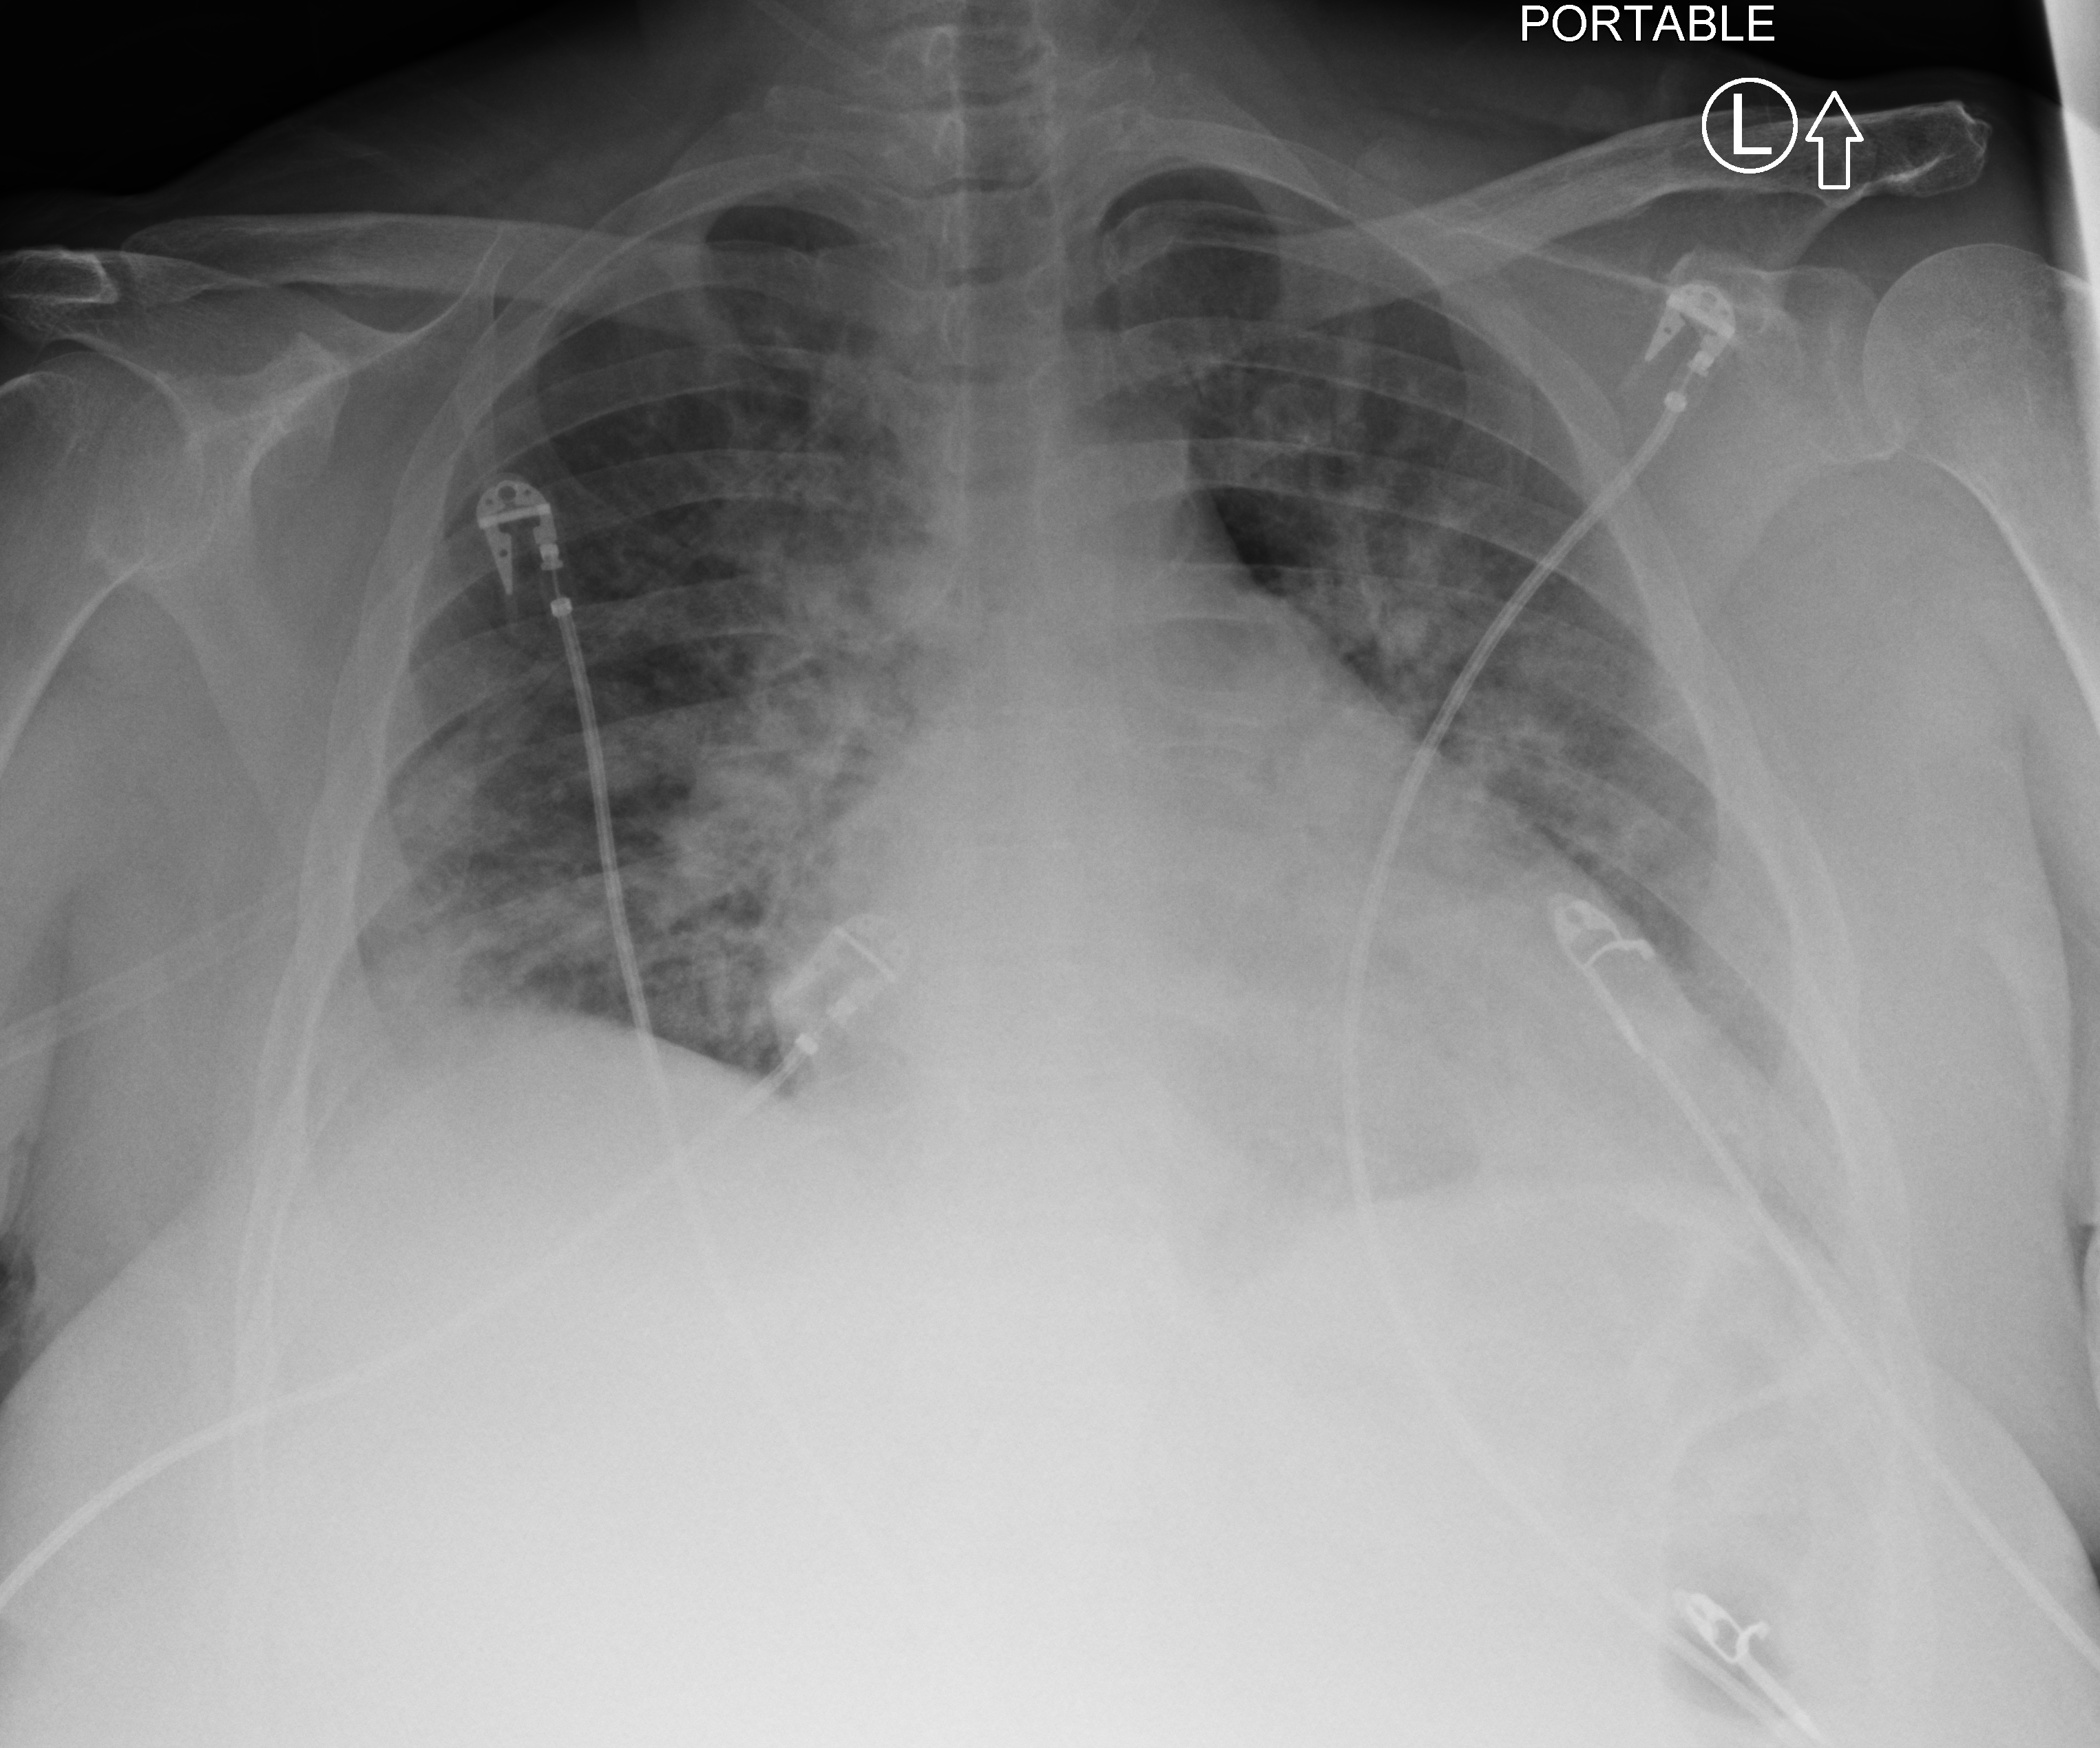
Bedside chest radiograph (computed radiography), anteroposterior (AP) projection. Female patient hospitalised with COVID-19, age 60–74 years.
Admission-level facts for this patient (not findings on this image; timing relative to this image not recorded): mechanically ventilated during this hospital stay: no; diabetes (admission record): yes; COPD (admission record): no.